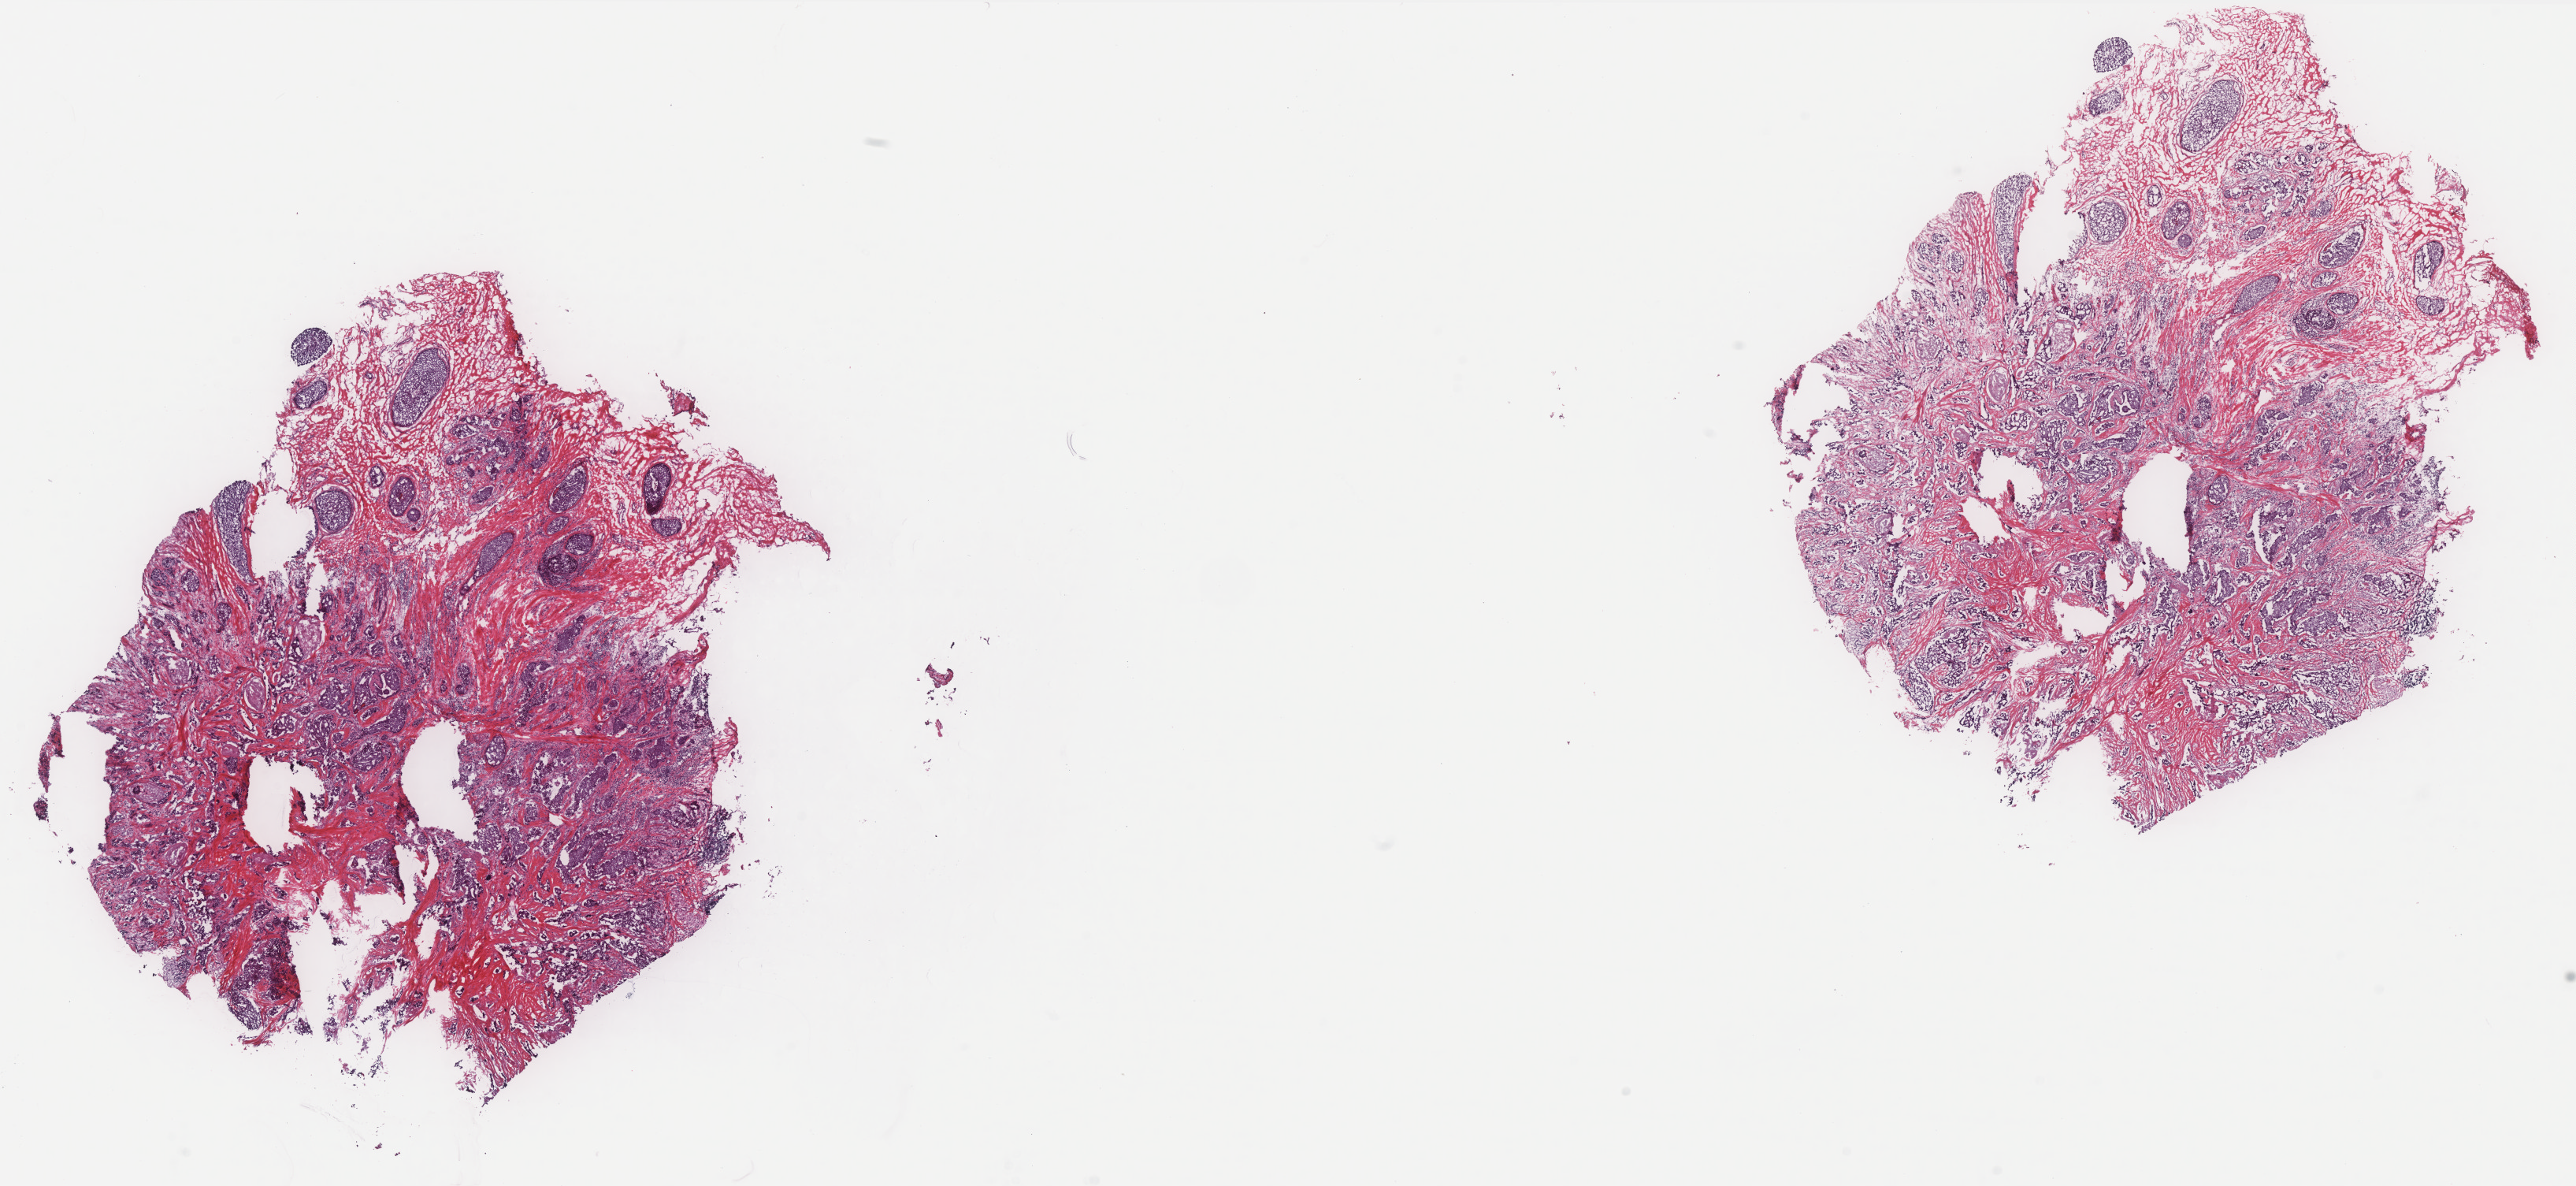
Digitized H&E-stained tissue section (whole slide), shown as a low-resolution overview of the whole scanned area (about 26.2 x 12.1 mm, acquisition: 40x scan). Frozen section from the top of the tissue portion. Sample: primary tumour, breast. Female patient; age at initial diagnosis 67 years. Slide review estimates, as recorded: tumour cells 70%, tumour nuclei 70%, normal cells 0%, stromal cells 30%, necrosis 0%. Inflammatory infiltration, as recorded: lymphocyte infiltration 2%, monocyte infiltration 1%, neutrophil infiltration 1%.
- AJCC pathologic stage: IIIA (7th edition)
- histologic diagnosis: Infiltrating duct carcinoma, NOS
- lymph nodes positive (case pathology): 7 of 16 examined